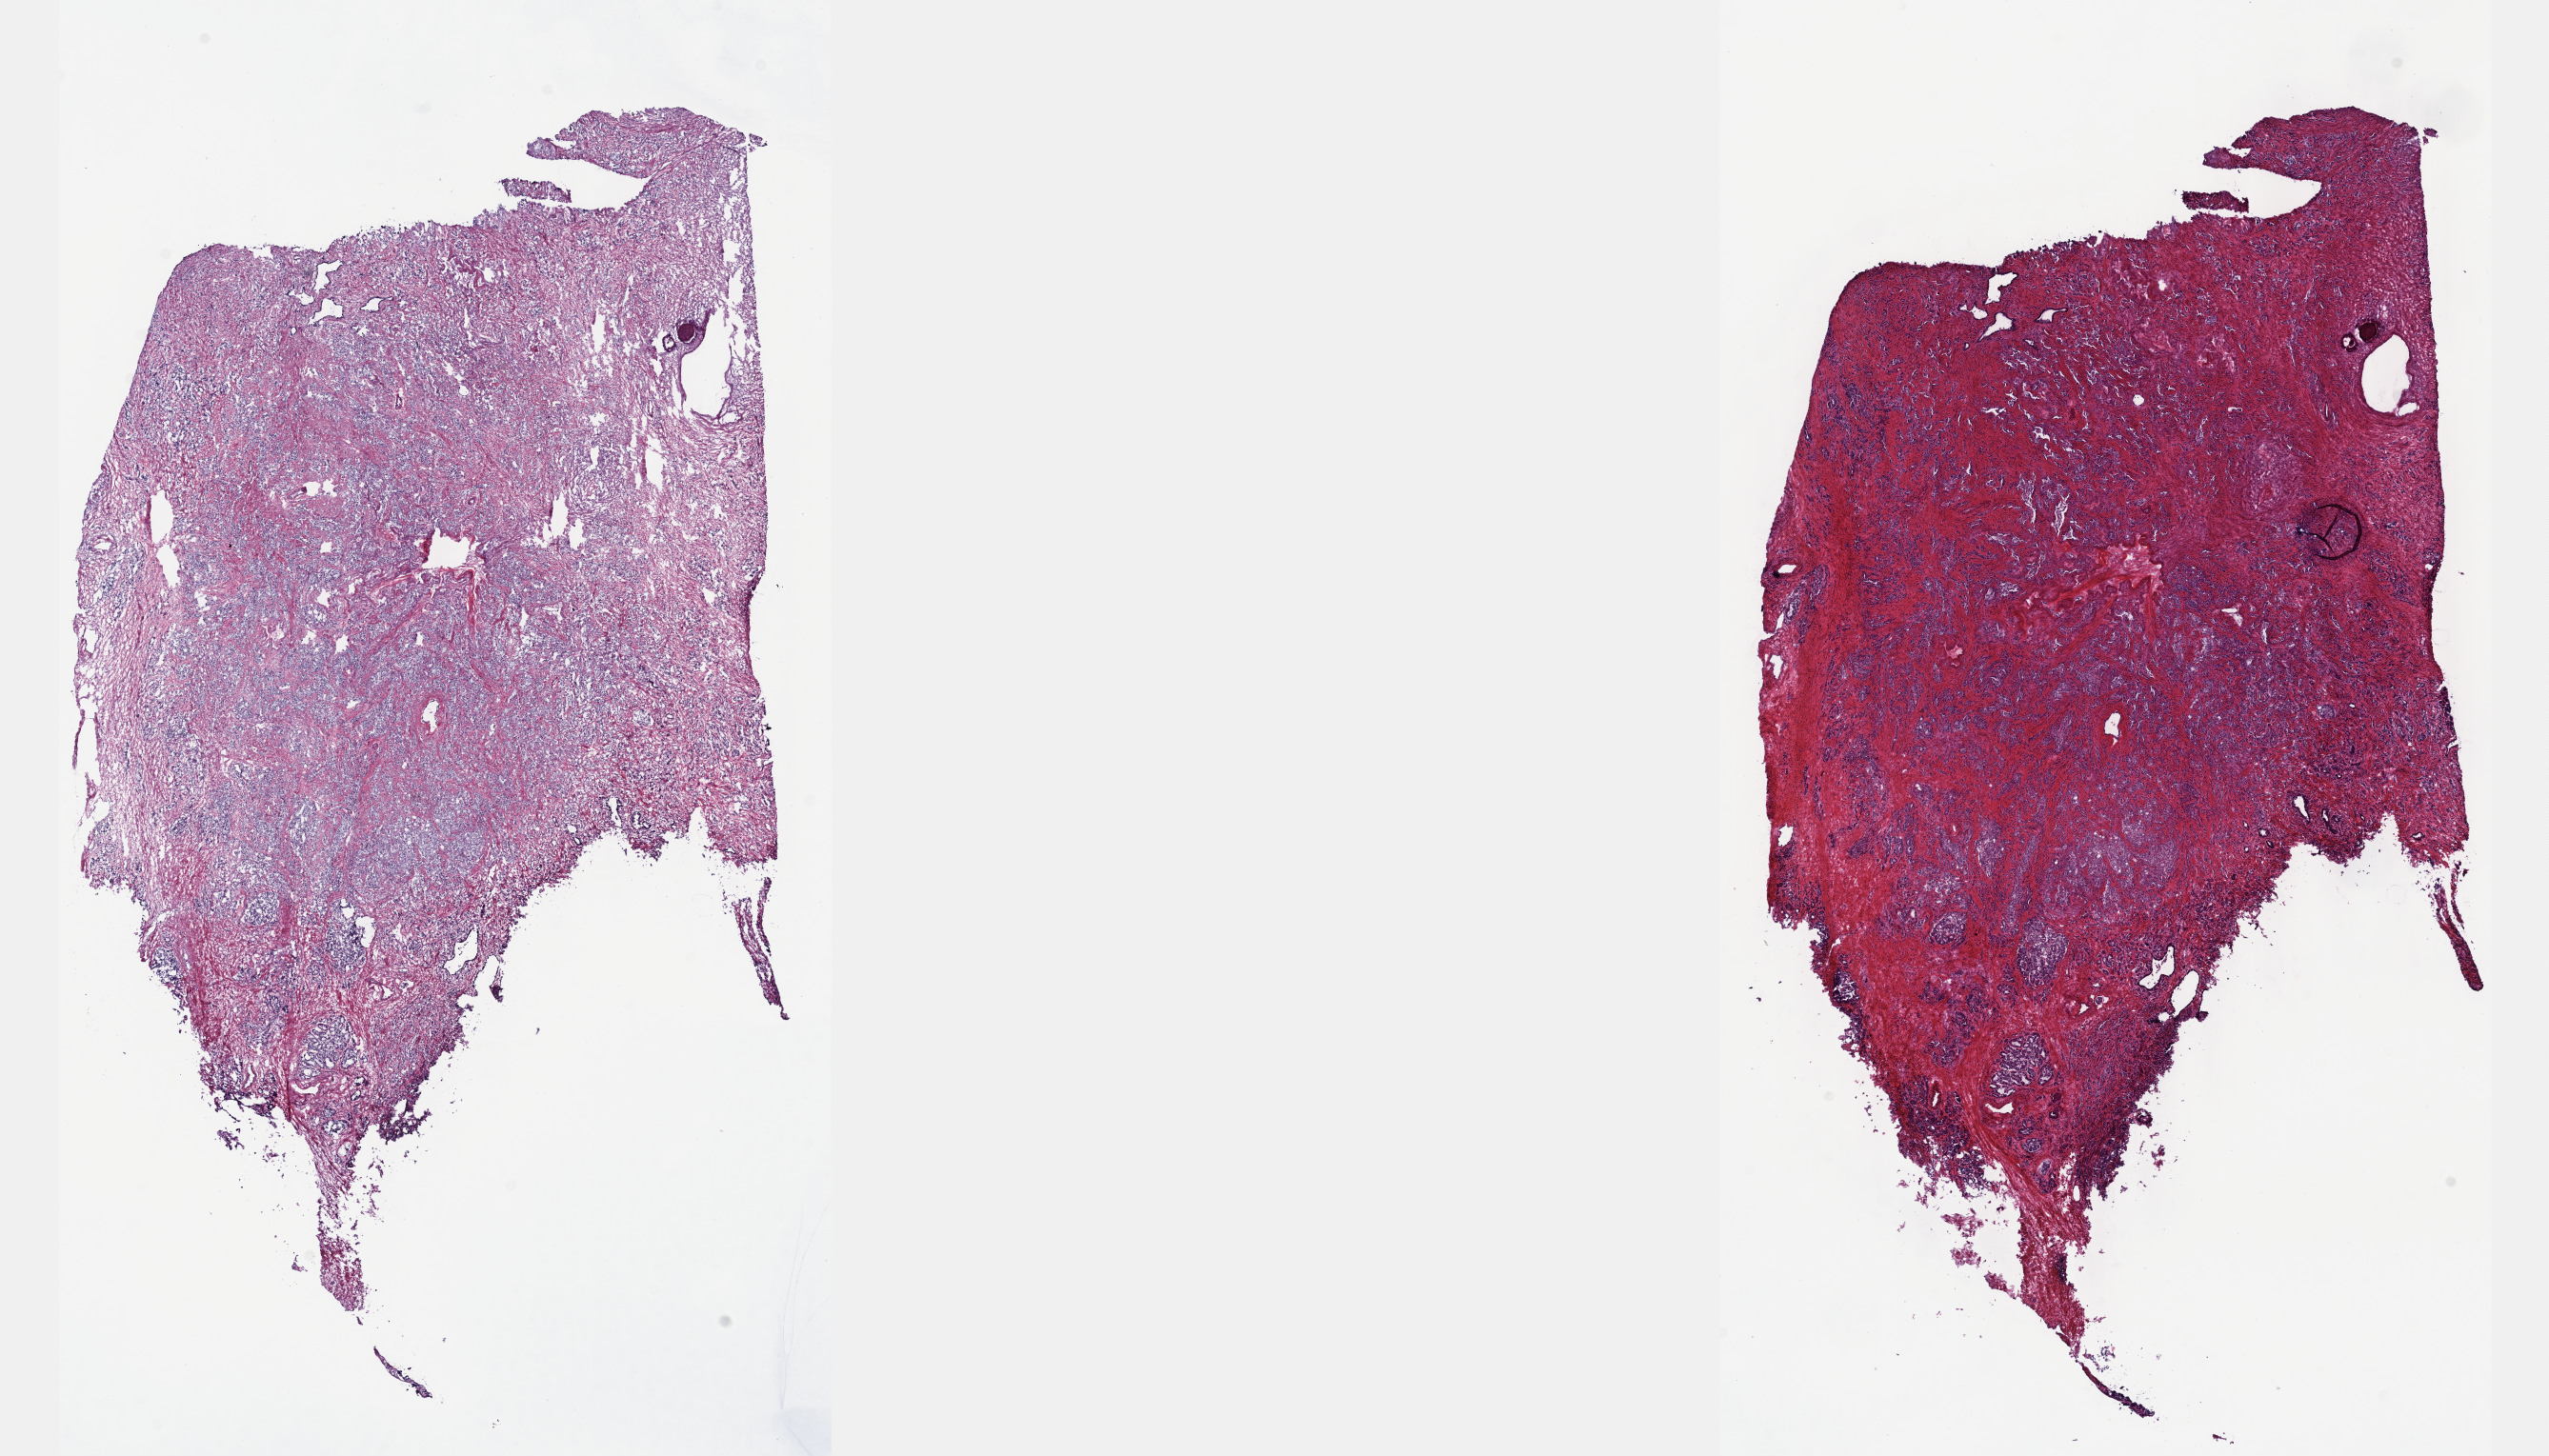
Digitized H&E tissue section (whole slide), whole scanned area (about 21.6 x 12.4 mm) shown as a low-resolution overview; frozen section from the top of the tissue portion; prostate, primary tumour sample. Male, age 68 years at initial diagnosis. Gleason score: 8 (4+4). Pathologist review of this section (percent, as recorded): tumour cells 80%, tumour nuclei 90%, normal cells 0%, stromal cells 20%, necrosis 0%. Inflammatory infiltration, as recorded: lymphocyte infiltration 0%, monocyte infiltration 0%, neutrophil infiltration 0%.
Pathologic diagnosis: Adenocarcinoma, NOS (prostate gland). Laterality: bilateral.